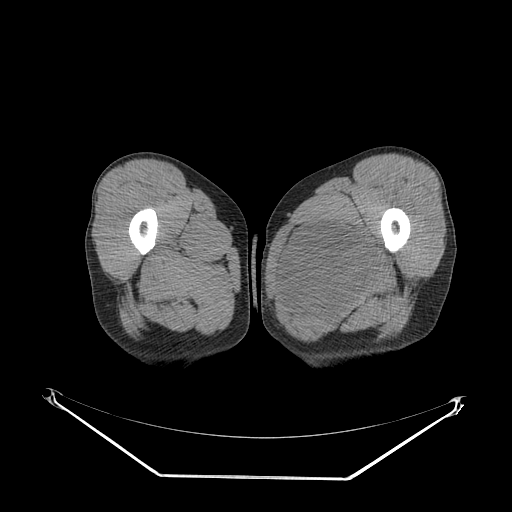
CT of an extremity soft-tissue mass (from a PET/CT study), one axial slice. Slice 28 of 267 in the series (ordered by position). Reconstruction kernel SOFT. 140 kVp. Soft-tissue window (W 400 / L 40 HU). 3.75 mm slice thickness. 512 × 512 image matrix. Male patient. From the clinical record (not read from this slice): histological type: pleiomorphic liposarcoma; grade: high; site of the primary tumour: left thigh.
Annotated regions visible in this slice (expert contour drawn on MRI and transferred to this co-registered scan by the dataset authors):
- gross tumour volume including surrounding oedema: bounding box [x1, y1, x2, y2] px = [283, 219, 384, 318]
- gross tumour volume (mass): [288, 224, 378, 312]